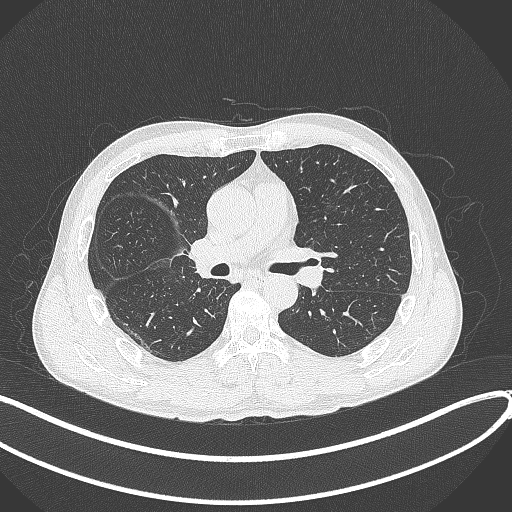
Chest CT, one axial slice. Slice 221 of 409 in the series (ordered by position). Reconstruction kernel B70f. Lung window (W 1500 / L -600 HU). 1 mm slice thickness. 512 × 512 image matrix, field of view 400 × 400 mm. Male patient, age 53 years. From the clinical record (not read from this slice): clinical TNM (as recorded): T1b N0 M0.
Annotated regions visible in this slice (bounding box drawn by a radiologist):
- lung tumour (recorded histology: squamous cell carcinoma): bounding box [x1, y1, x2, y2] px = [190, 232, 223, 282]